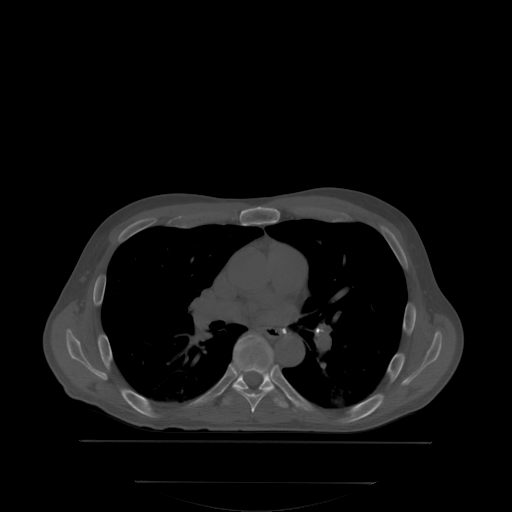
CT including the spine, one axial slice. Position 232 of 350 along the scan axis. Bone window (W 1800 / L 400 HU). 2.5 mm slice thickness. 512 × 512 image matrix. Patient: male, 58 years. Case-level facts recorded for this patient, not image findings: primary cancer: prostate.
Outlined on this slice (semi-automatically segmented with operator editing):
- T6 vertebra: bounding box (x1, y1, x2, y2) in pixels: (232, 387, 274, 412)
- T7 vertebra: (224, 334, 287, 406)